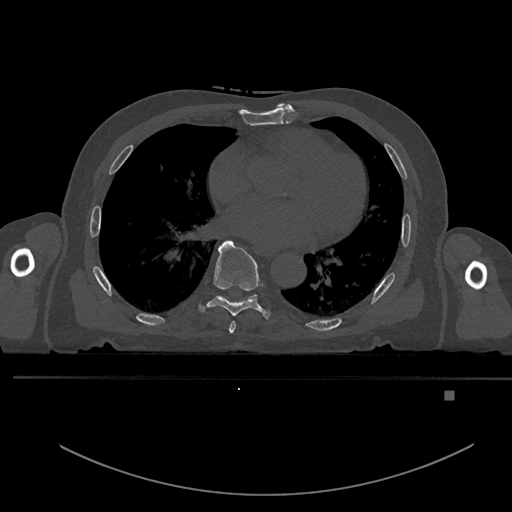
CT including the spine, one axial slice. Slice 251 of 969 in the series (ordered by position). Bone window (W 1800 / L 400 HU). 0.5 mm slice thickness. 512 × 512 image matrix, field of view 456 × 456 mm. Patient: male, 82 years. From the clinical record (not read from this slice): primary cancer: prostate; vertebrae with lytic lesions (as recorded): T11, T9, T8, T2.
Structures marked on this image (semi-automatic segmentation, software-assisted and operator-edited):
- T6 vertebra: bounding box (x1, y1, x2, y2) in pixels: (229, 321, 236, 334)
- T7 vertebra: (199, 240, 271, 319)
- T8 vertebra: (220, 295, 258, 303)